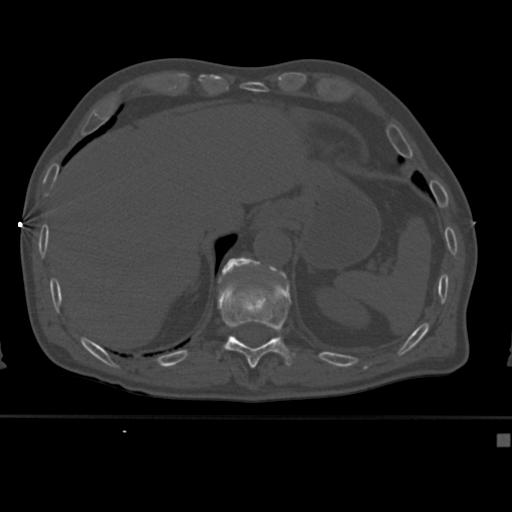
CT including the spine, one axial slice. Slice 208 of 430 in the series (ordered by position). Reconstruction kernel Br40s. 120 kVp. Bone window (W 1800 / L 400 HU). 1.5 mm slice thickness. 512 × 512 image matrix, field of view 337 × 337 mm. Male patient, age 64 years. Case-level facts recorded for this patient, not image findings: primary cancer: uterus.
Annotated regions visible in this slice (semi-automatically segmented with operator editing):
- T11 vertebra: box from (x=217, y=265) to (x=296, y=368) px
- T12 vertebra: (x=221, y=257)–(x=284, y=277)